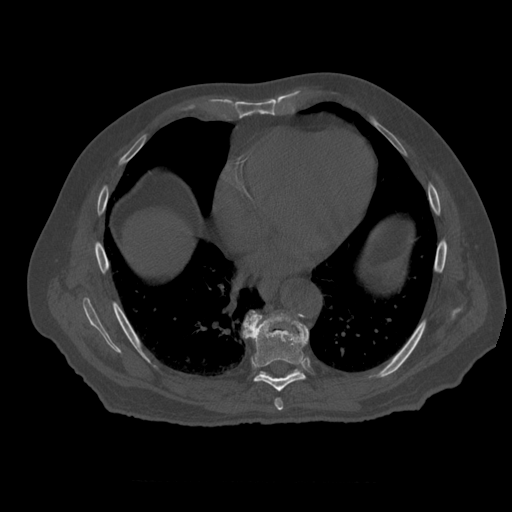
CT including the spine, one axial slice. Position 338 of 399 along the scan axis. Reconstruction kernel STANDARD. 120 kVp. Bone window (W 1800 / L 400 HU). 512 × 512 image matrix. Patient age 73 years. Case-level facts recorded for this patient, not image findings: primary cancer: prostate; vertebrae with lytic lesions (as recorded): L2.
Structures marked on this image (semi-automatic segmentation, software-assisted and operator-edited):
- T7 vertebra: box from (x=275, y=398) to (x=283, y=412) px
- T8 vertebra: (x=243, y=312)–(x=310, y=392)
- T9 vertebra: (x=249, y=311)–(x=300, y=378)